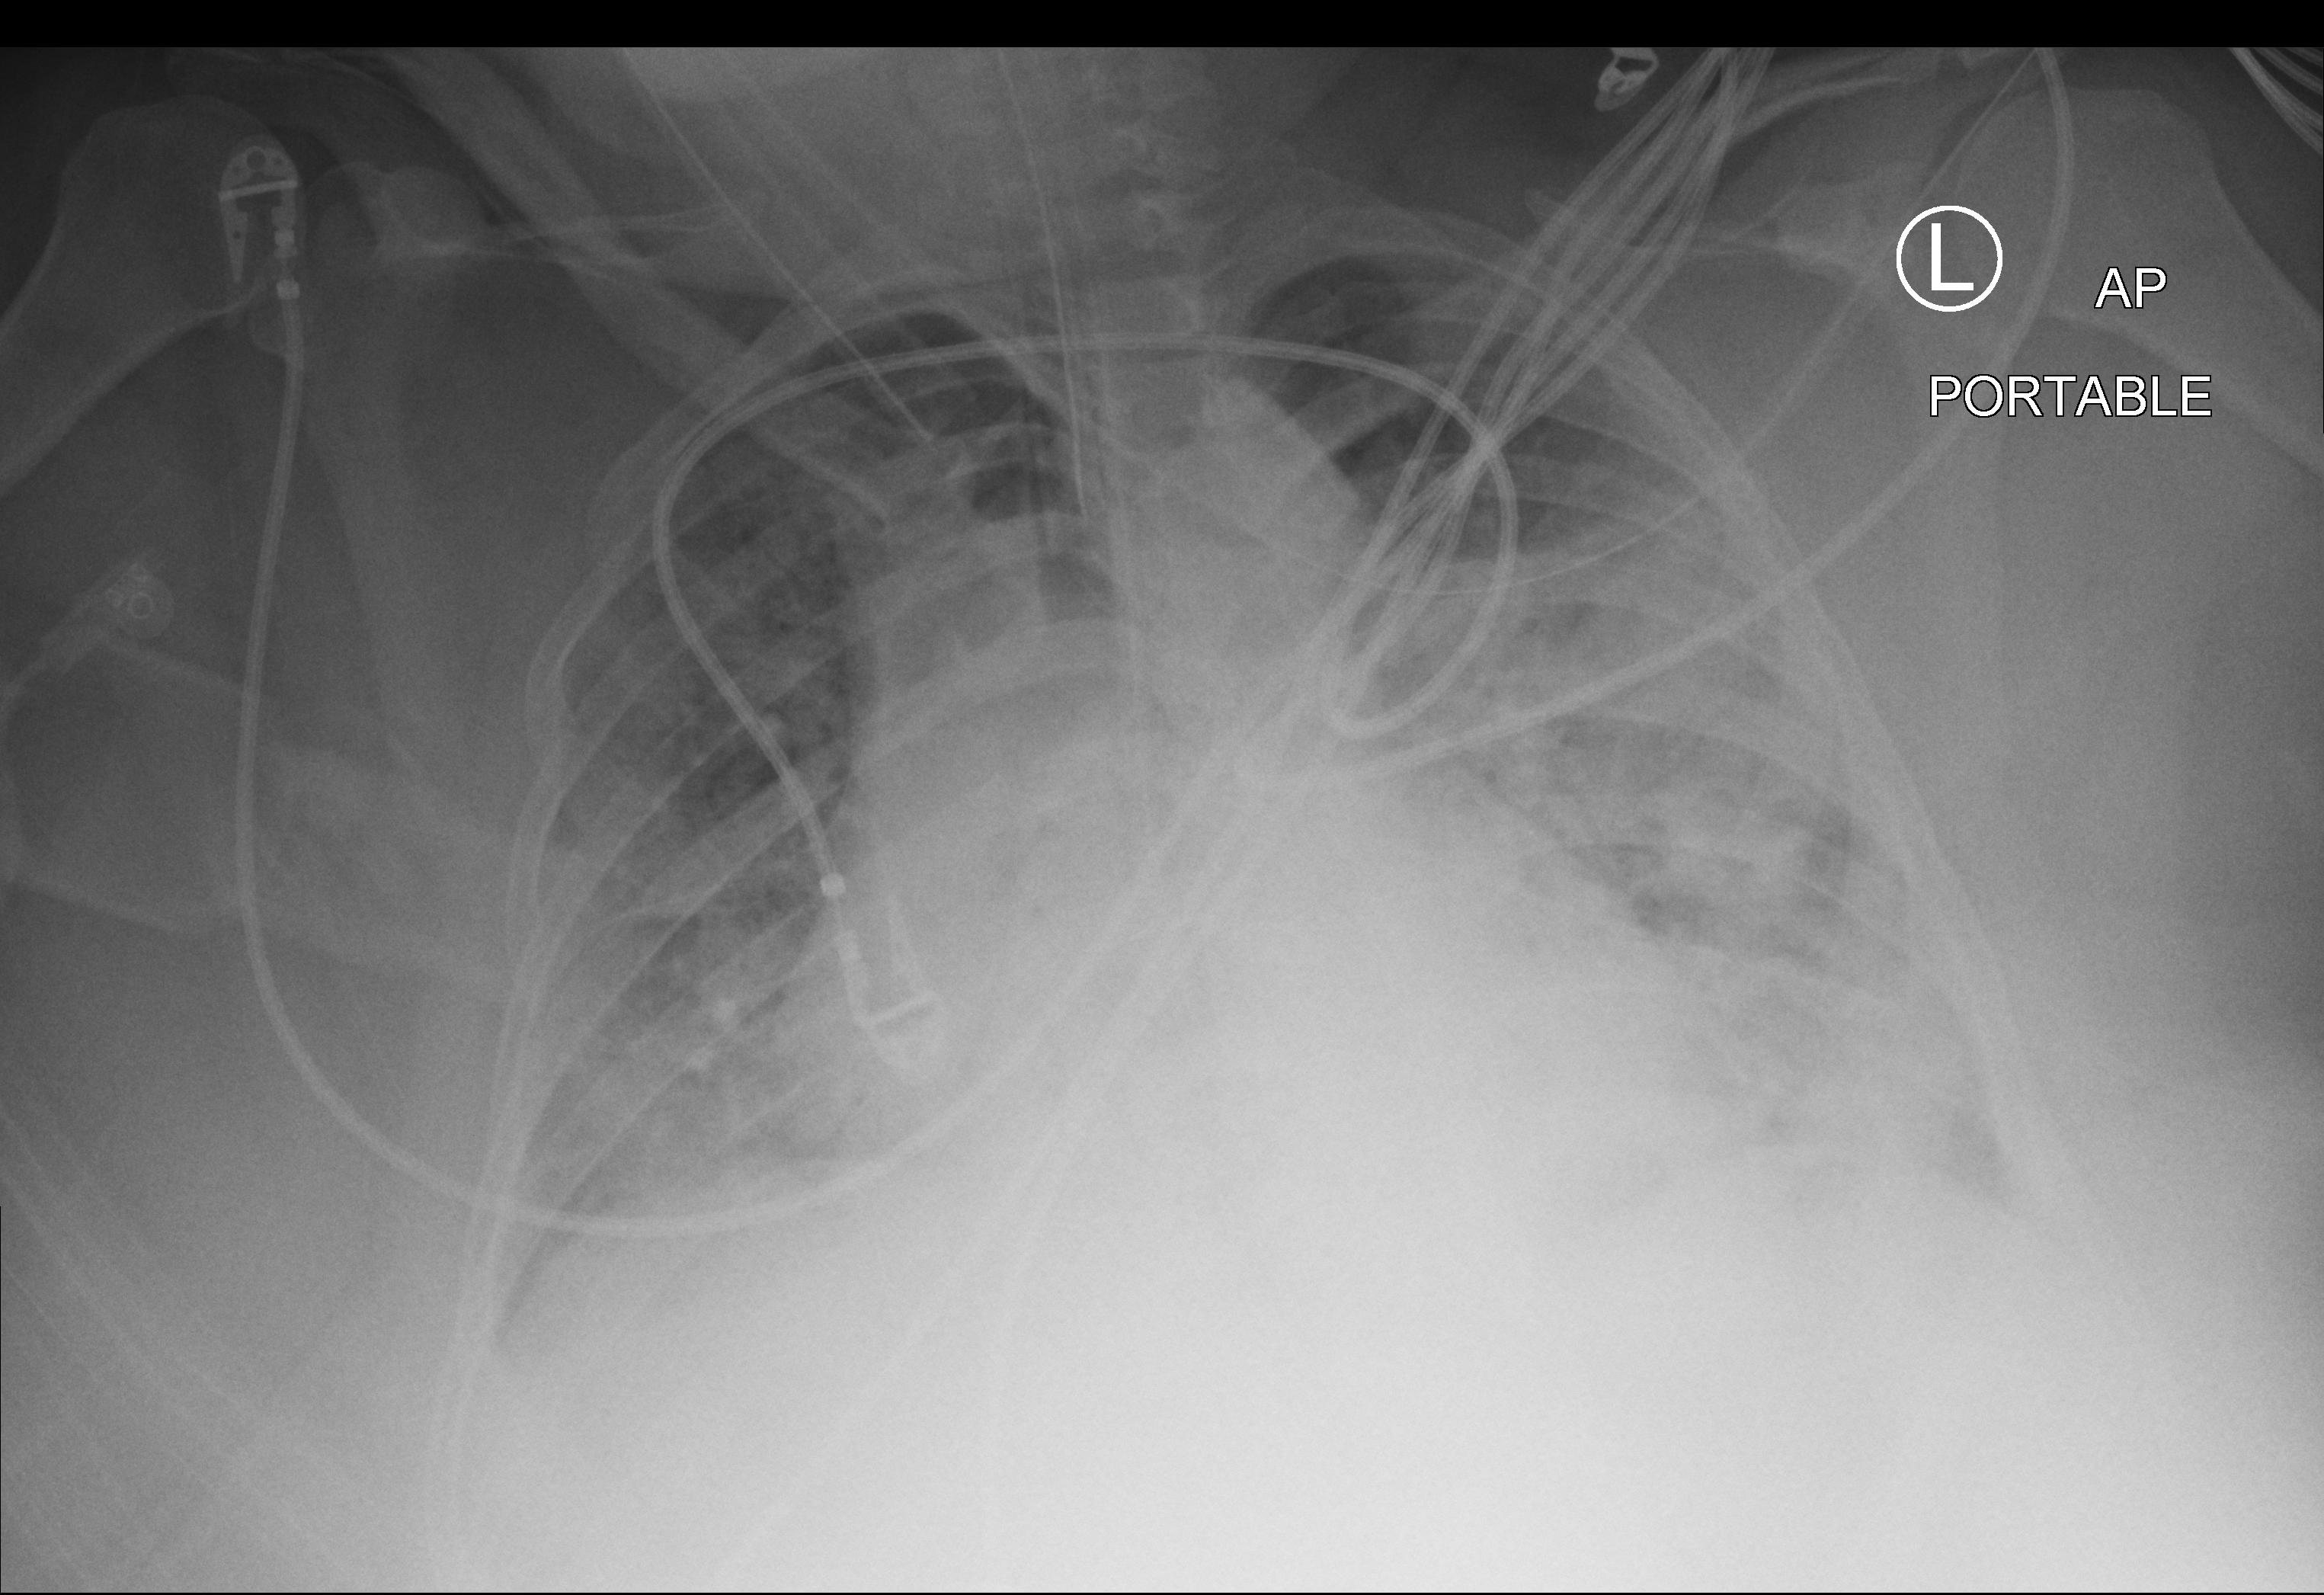
Chest X-ray (portable), anteroposterior (AP) projection. Patient hospitalised with COVID-19; female, aged 18–59 years.
Hospital-stay facts (about this admission, not read from this image; timing relative to this image not recorded):
- length of hospital stay: 23 days